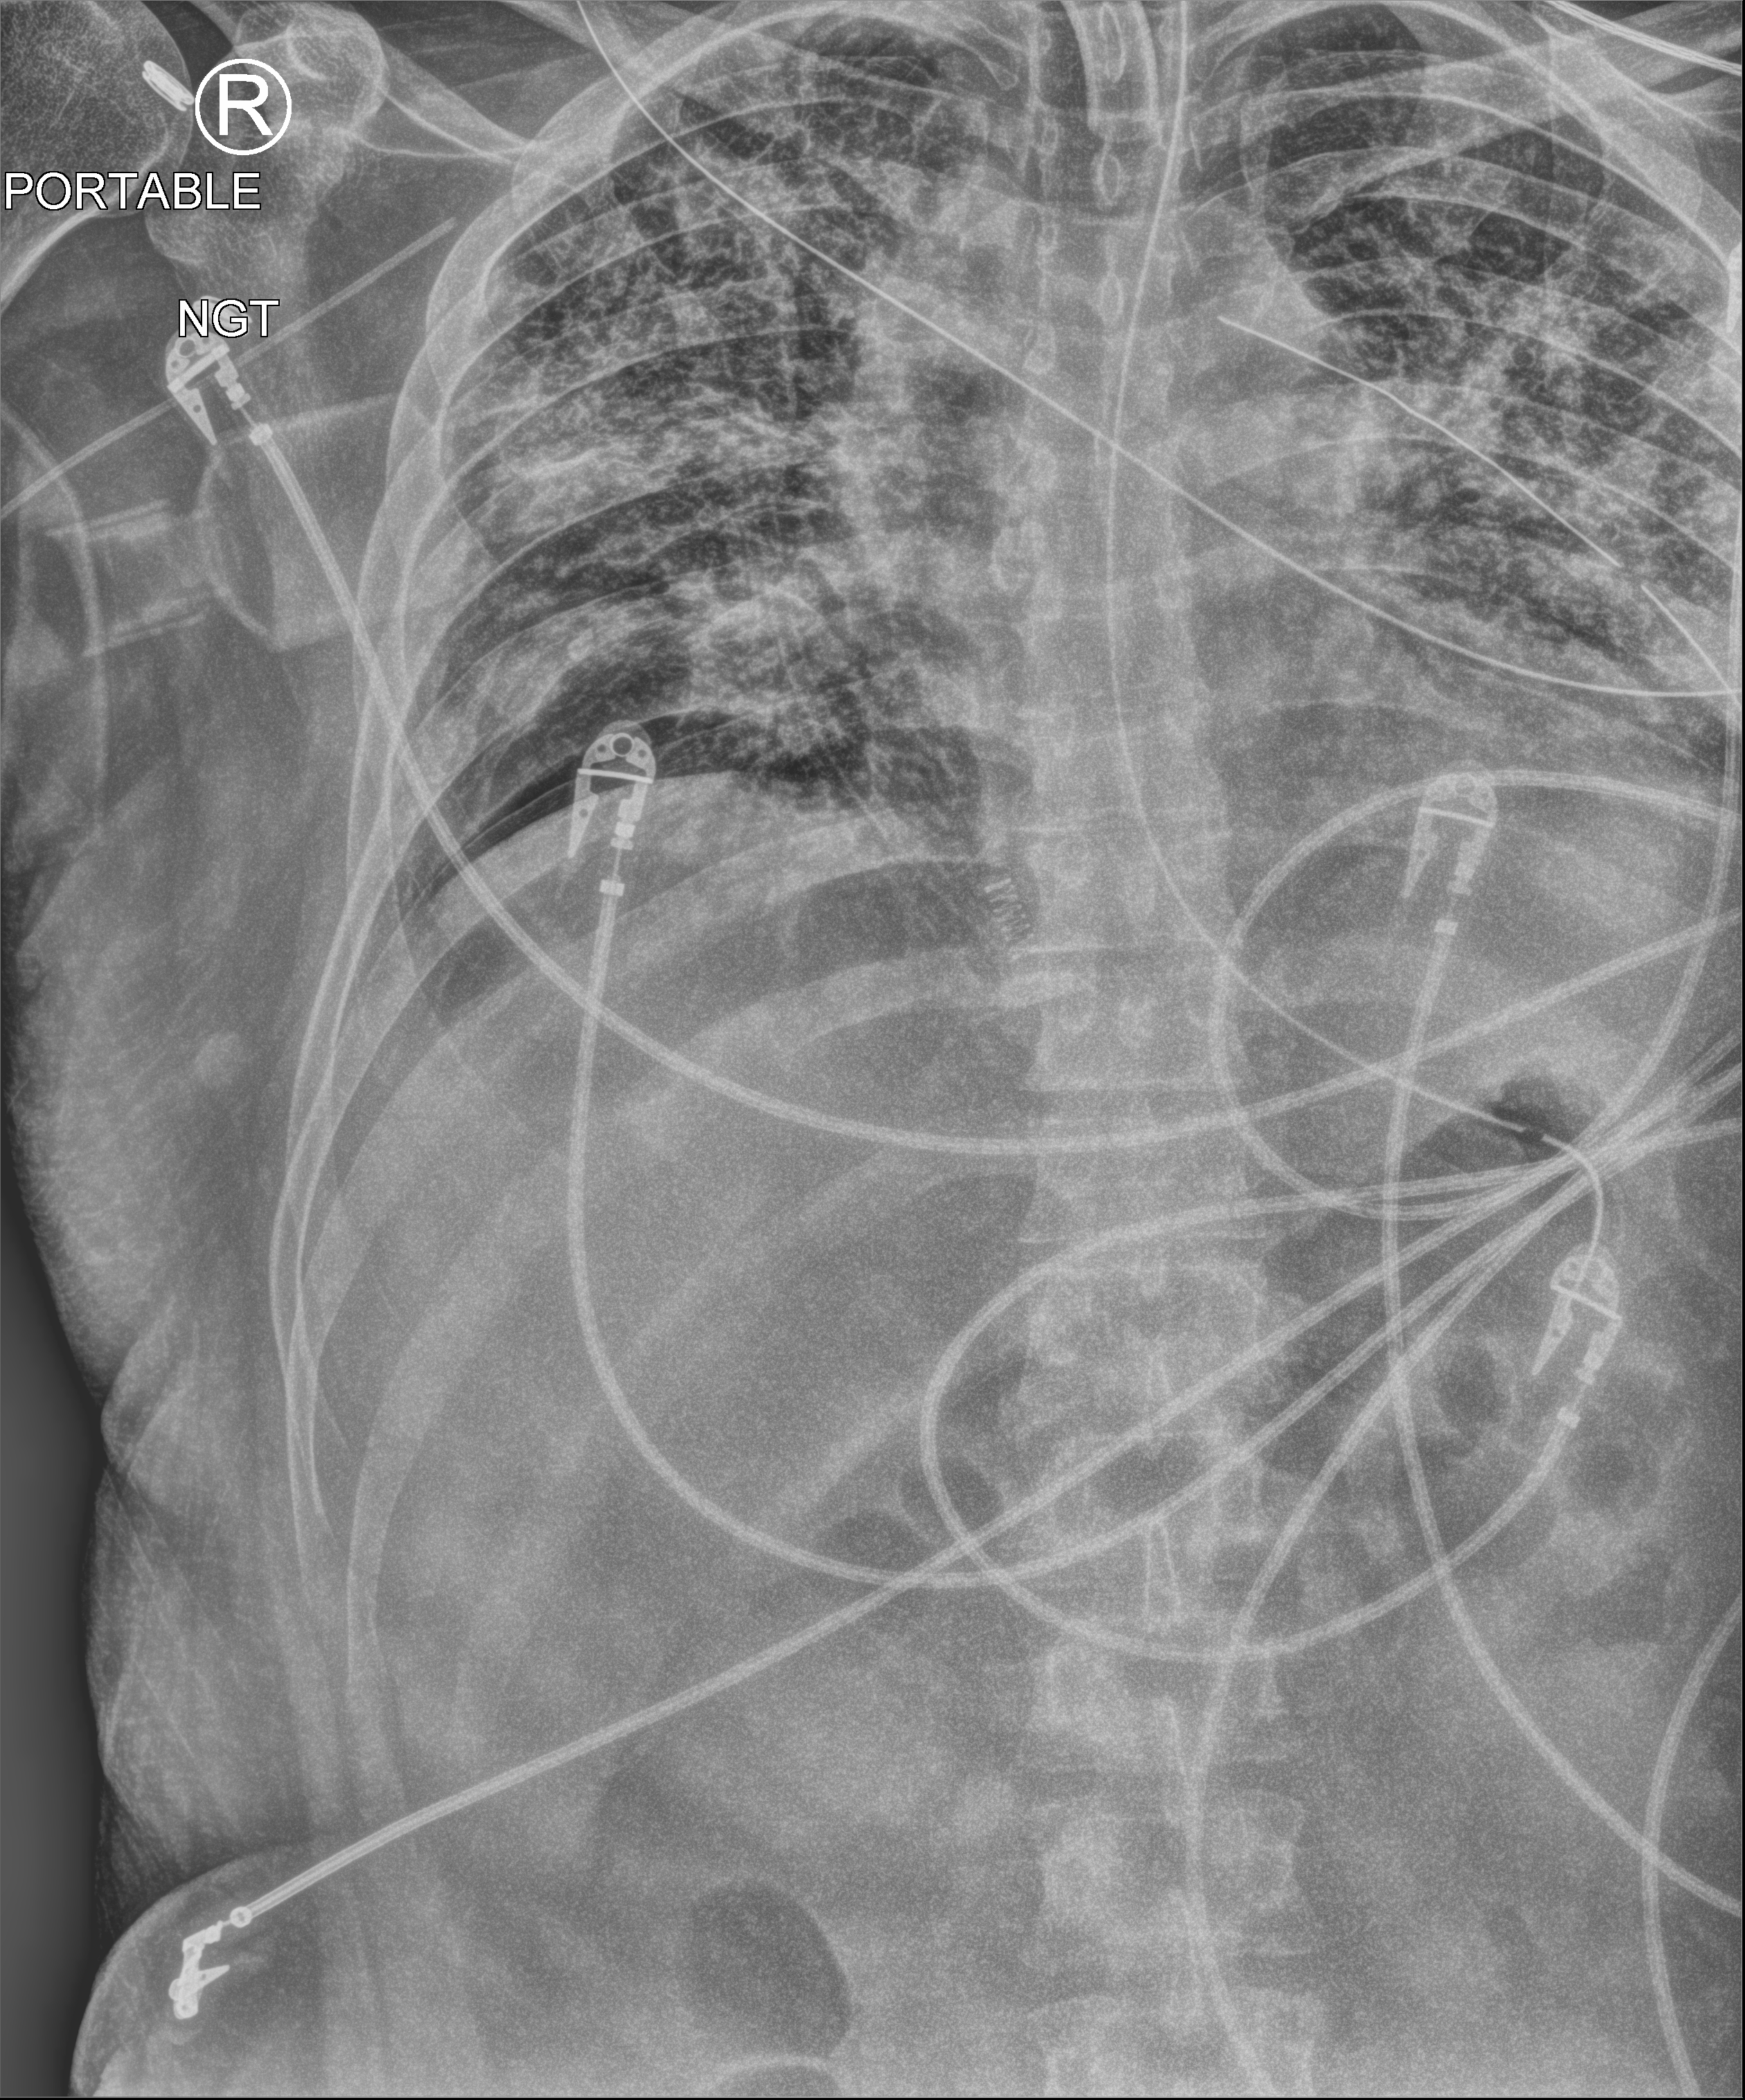
Portable chest radiograph; anteroposterior (AP) projection. Patient hospitalised with COVID-19; male, aged 18–59 years.
Hospital-stay facts (about this admission, not read from this image; timing relative to this image not recorded): hypertension (admission record): yes; mechanically ventilated during this hospital stay: yes; admitted to intensive care during this hospital stay: yes.